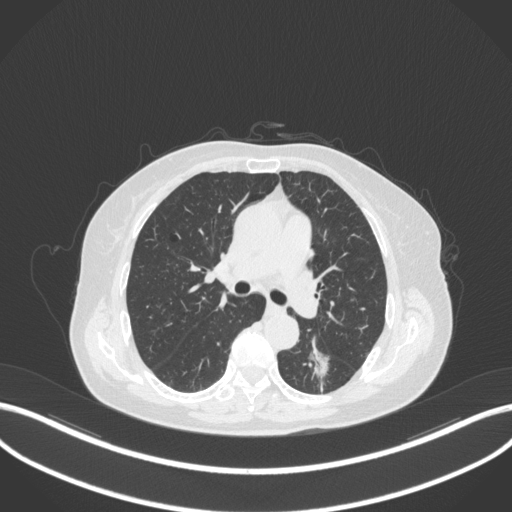
Chest CT, one axial slice. Position 179 of 352 along the scan axis. Lung window (W 1500 / L -600 HU). 1 mm slice thickness. 512 × 512 image matrix, field of view 400 × 400 mm. Female patient, age 70 years. From the clinical record (not read from this slice): clinical TNM (as recorded): T1c N0 M0.
Structures marked on this image (rectangle marked by the reading radiologist):
- lung tumour (recorded histology: adenocarcinoma): bounding box <299,336,334,385> (left, top, right, bottom; pixels)